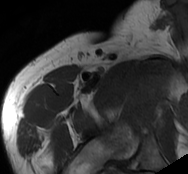
MRI of an extremity soft-tissue mass, one axial slice; position 74 of 93 along the scan axis; MR volume resampled by the dataset authors to the PET/CT grid (not the native acquisition matrix); 188 × 174 image matrix. Male patient. Case-level facts recorded for this patient, not image findings: histological type: undifferentiated - pleiomorphic; grade: high; site of the primary tumour: right thigh.
Structures marked on this image (expert contour drawn on MRI and transferred to this co-registered scan by the dataset authors):
- gross tumour volume including surrounding oedema: box from (x=123, y=64) to (x=174, y=104) px
- gross tumour volume (mass): (x=129, y=72)–(x=162, y=100)